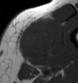
MRI of an extremity soft-tissue mass, one axial slice. Slice 24 of 43 in the series (ordered by position). MR volume resampled by the dataset authors to the PET/CT grid (not the native acquisition matrix). 78 × 83 image matrix, field of view 76 × 81 mm. Male patient. From the clinical record (not read from this slice): histological type: pleiomorphic leiomyosarcoma; grade: high; site of the primary tumour: left thigh.
Structures marked on this image (expert contour drawn on MRI and transferred to this co-registered scan by the dataset authors):
- gross tumour volume including surrounding oedema: bounding box <18,19,58,64> (left, top, right, bottom; pixels)
- gross tumour volume (mass): <20,22,53,61>